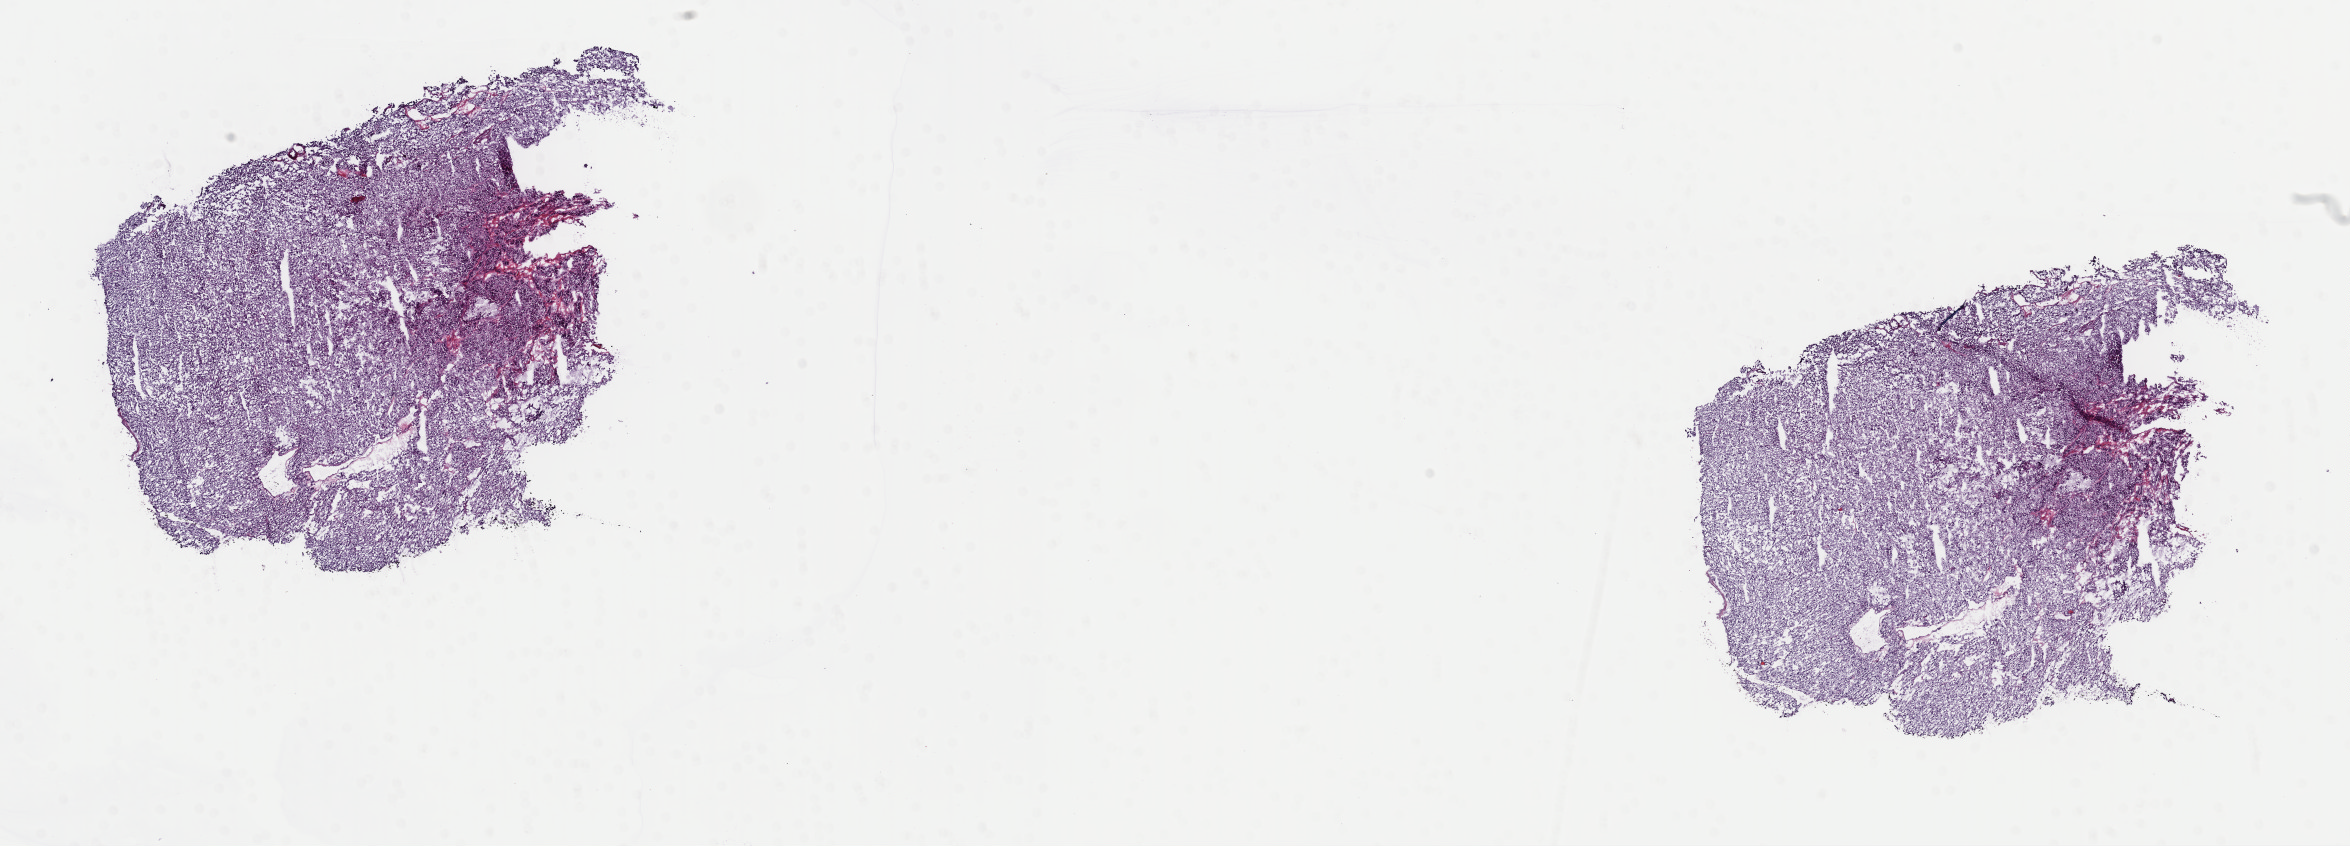
Digitized Hematoxylin and eosin (H&E) stained tissue section (whole slide) — whole scanned area (about 18.6 x 6.7 mm, from a 40x scan) shown as a low-resolution overview, frozen section from the top of the tissue portion, sample: primary tumour, adrenal gland. Patient: female, age at initial diagnosis 78 years.
Diagnosis: Pheochromocytoma, malignant.